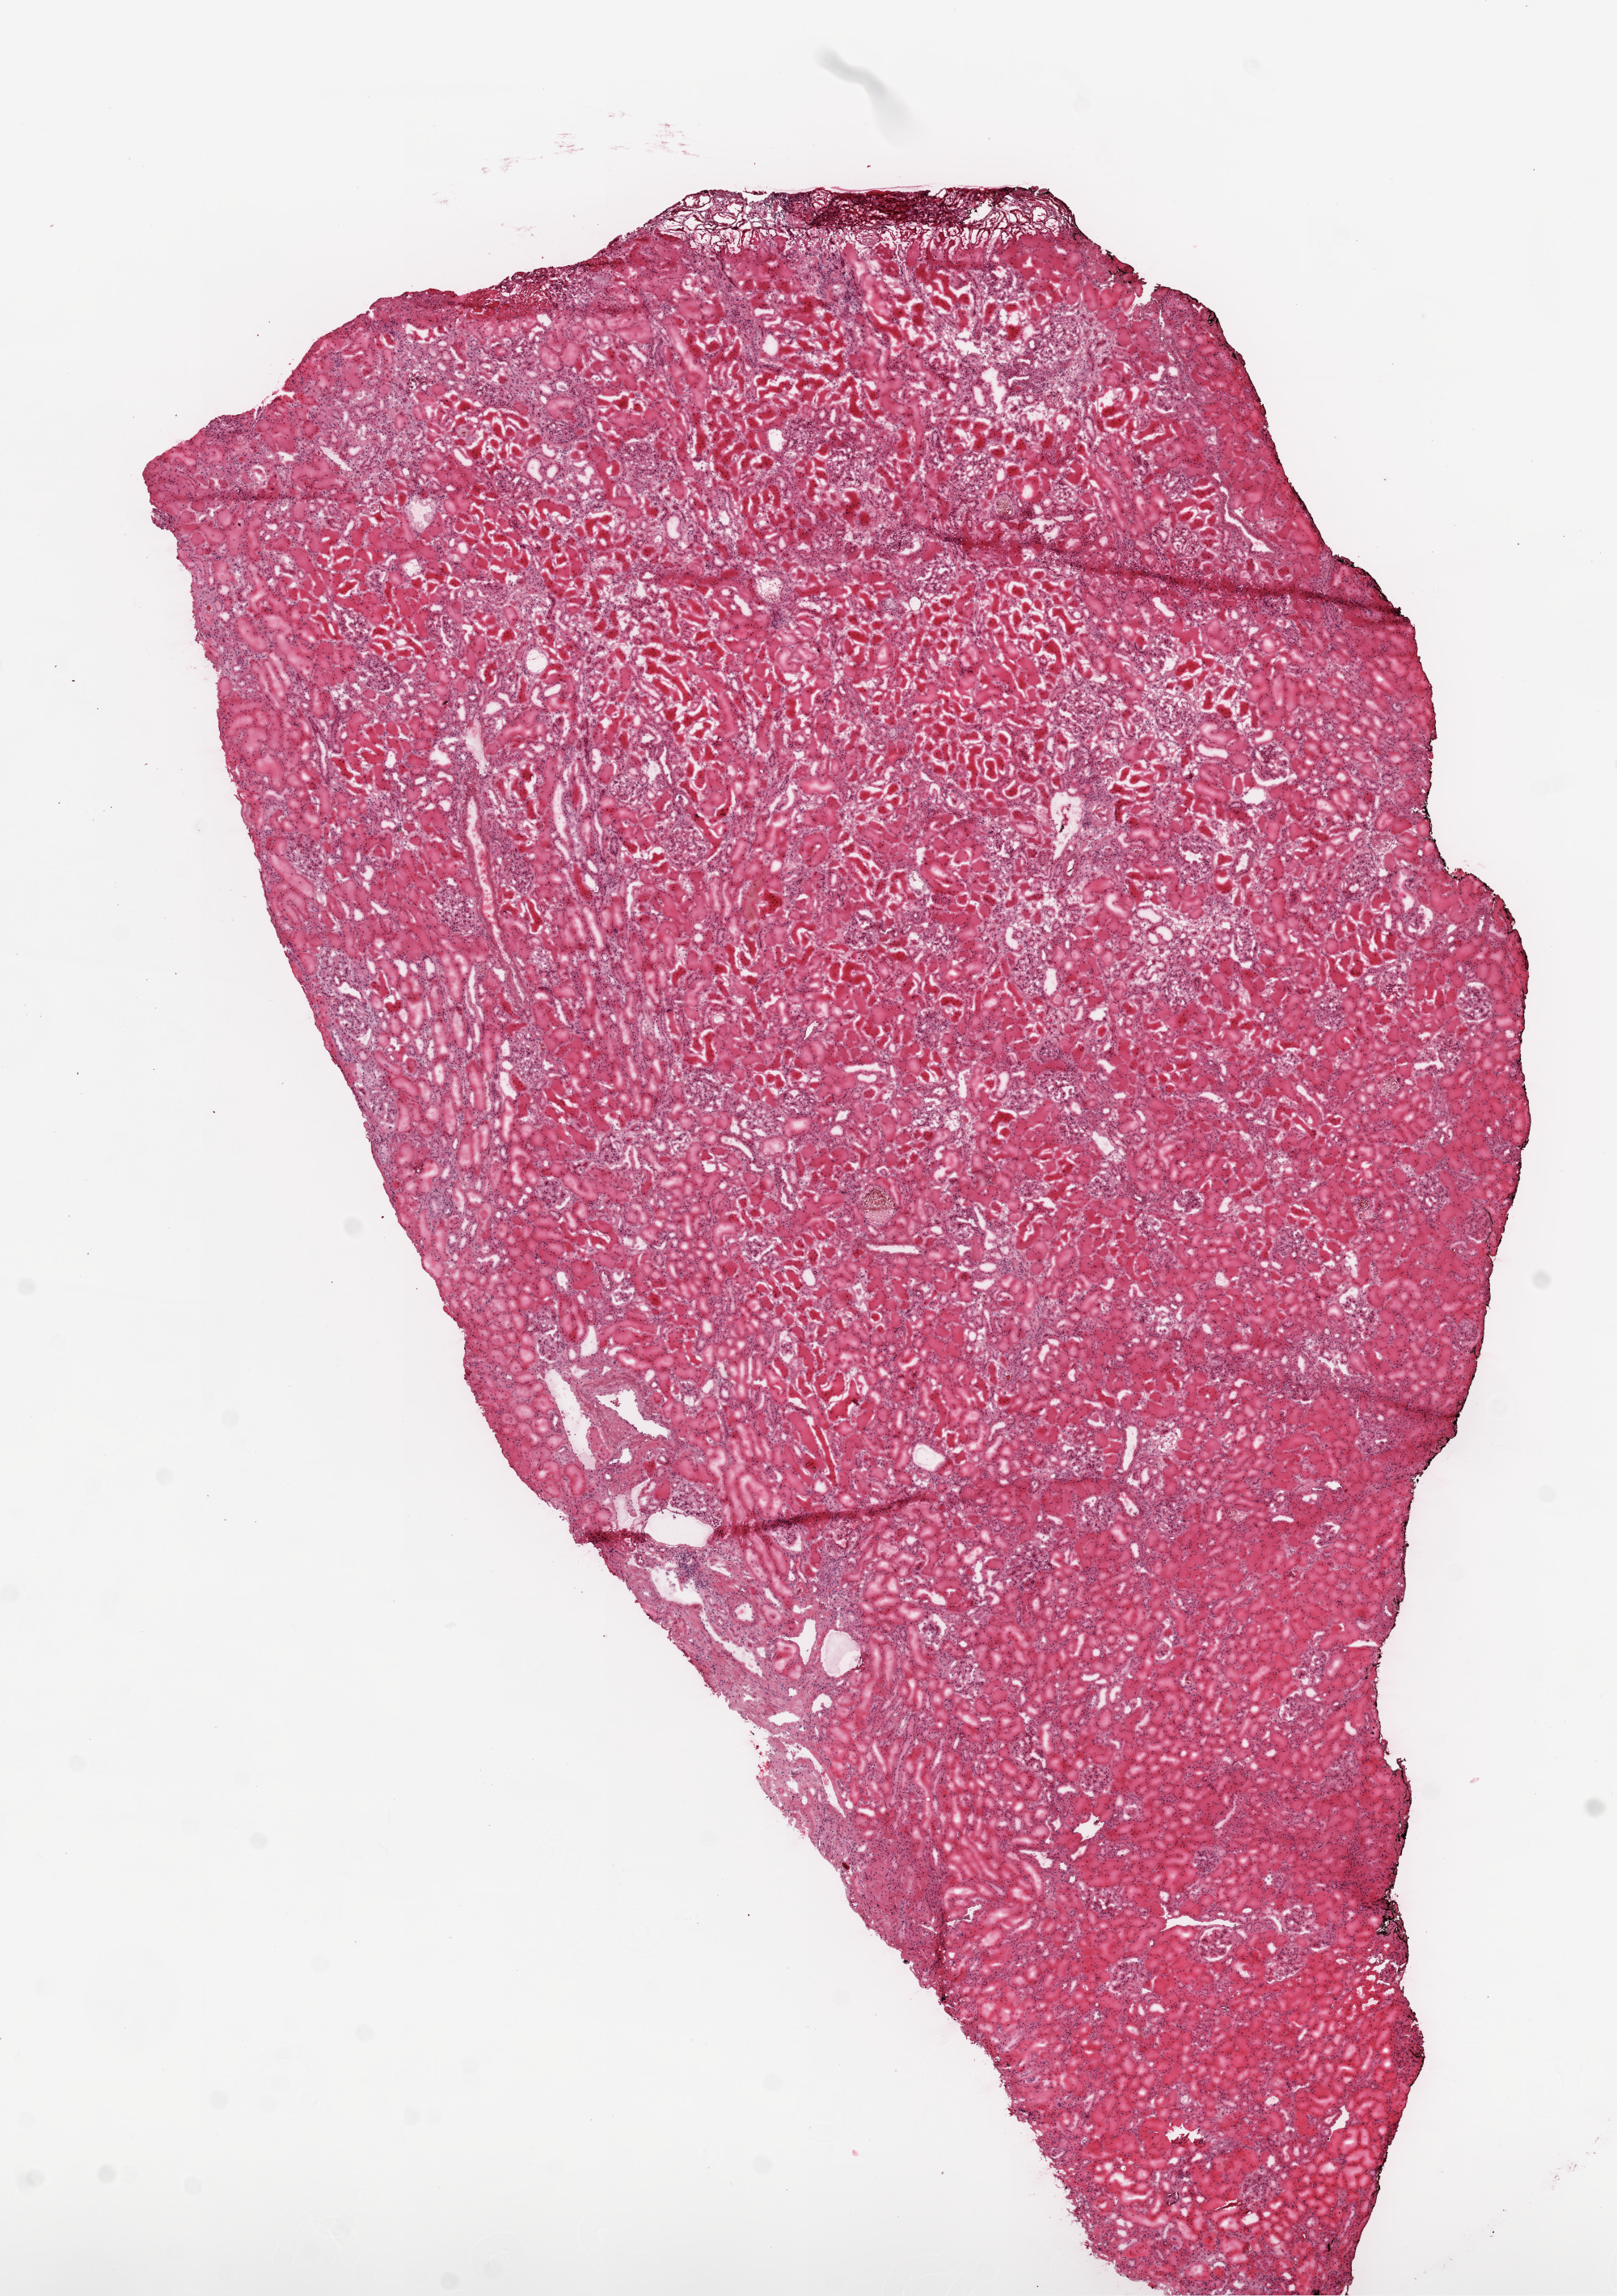
Digitized H&E tissue section (whole slide), low-resolution overview of the scanned area, about 8.0 x 11.4 mm (acquisition: 20x scan), frozen section from the top of the tissue portion, sample: solid tissue normal (non-tumour tissue), kidney. Male, age 69 years at initial diagnosis.
• this section: solid tissue normal (non-tumour) sample from the same patient
• patient diagnosis: Clear cell adenocarcinoma, NOS